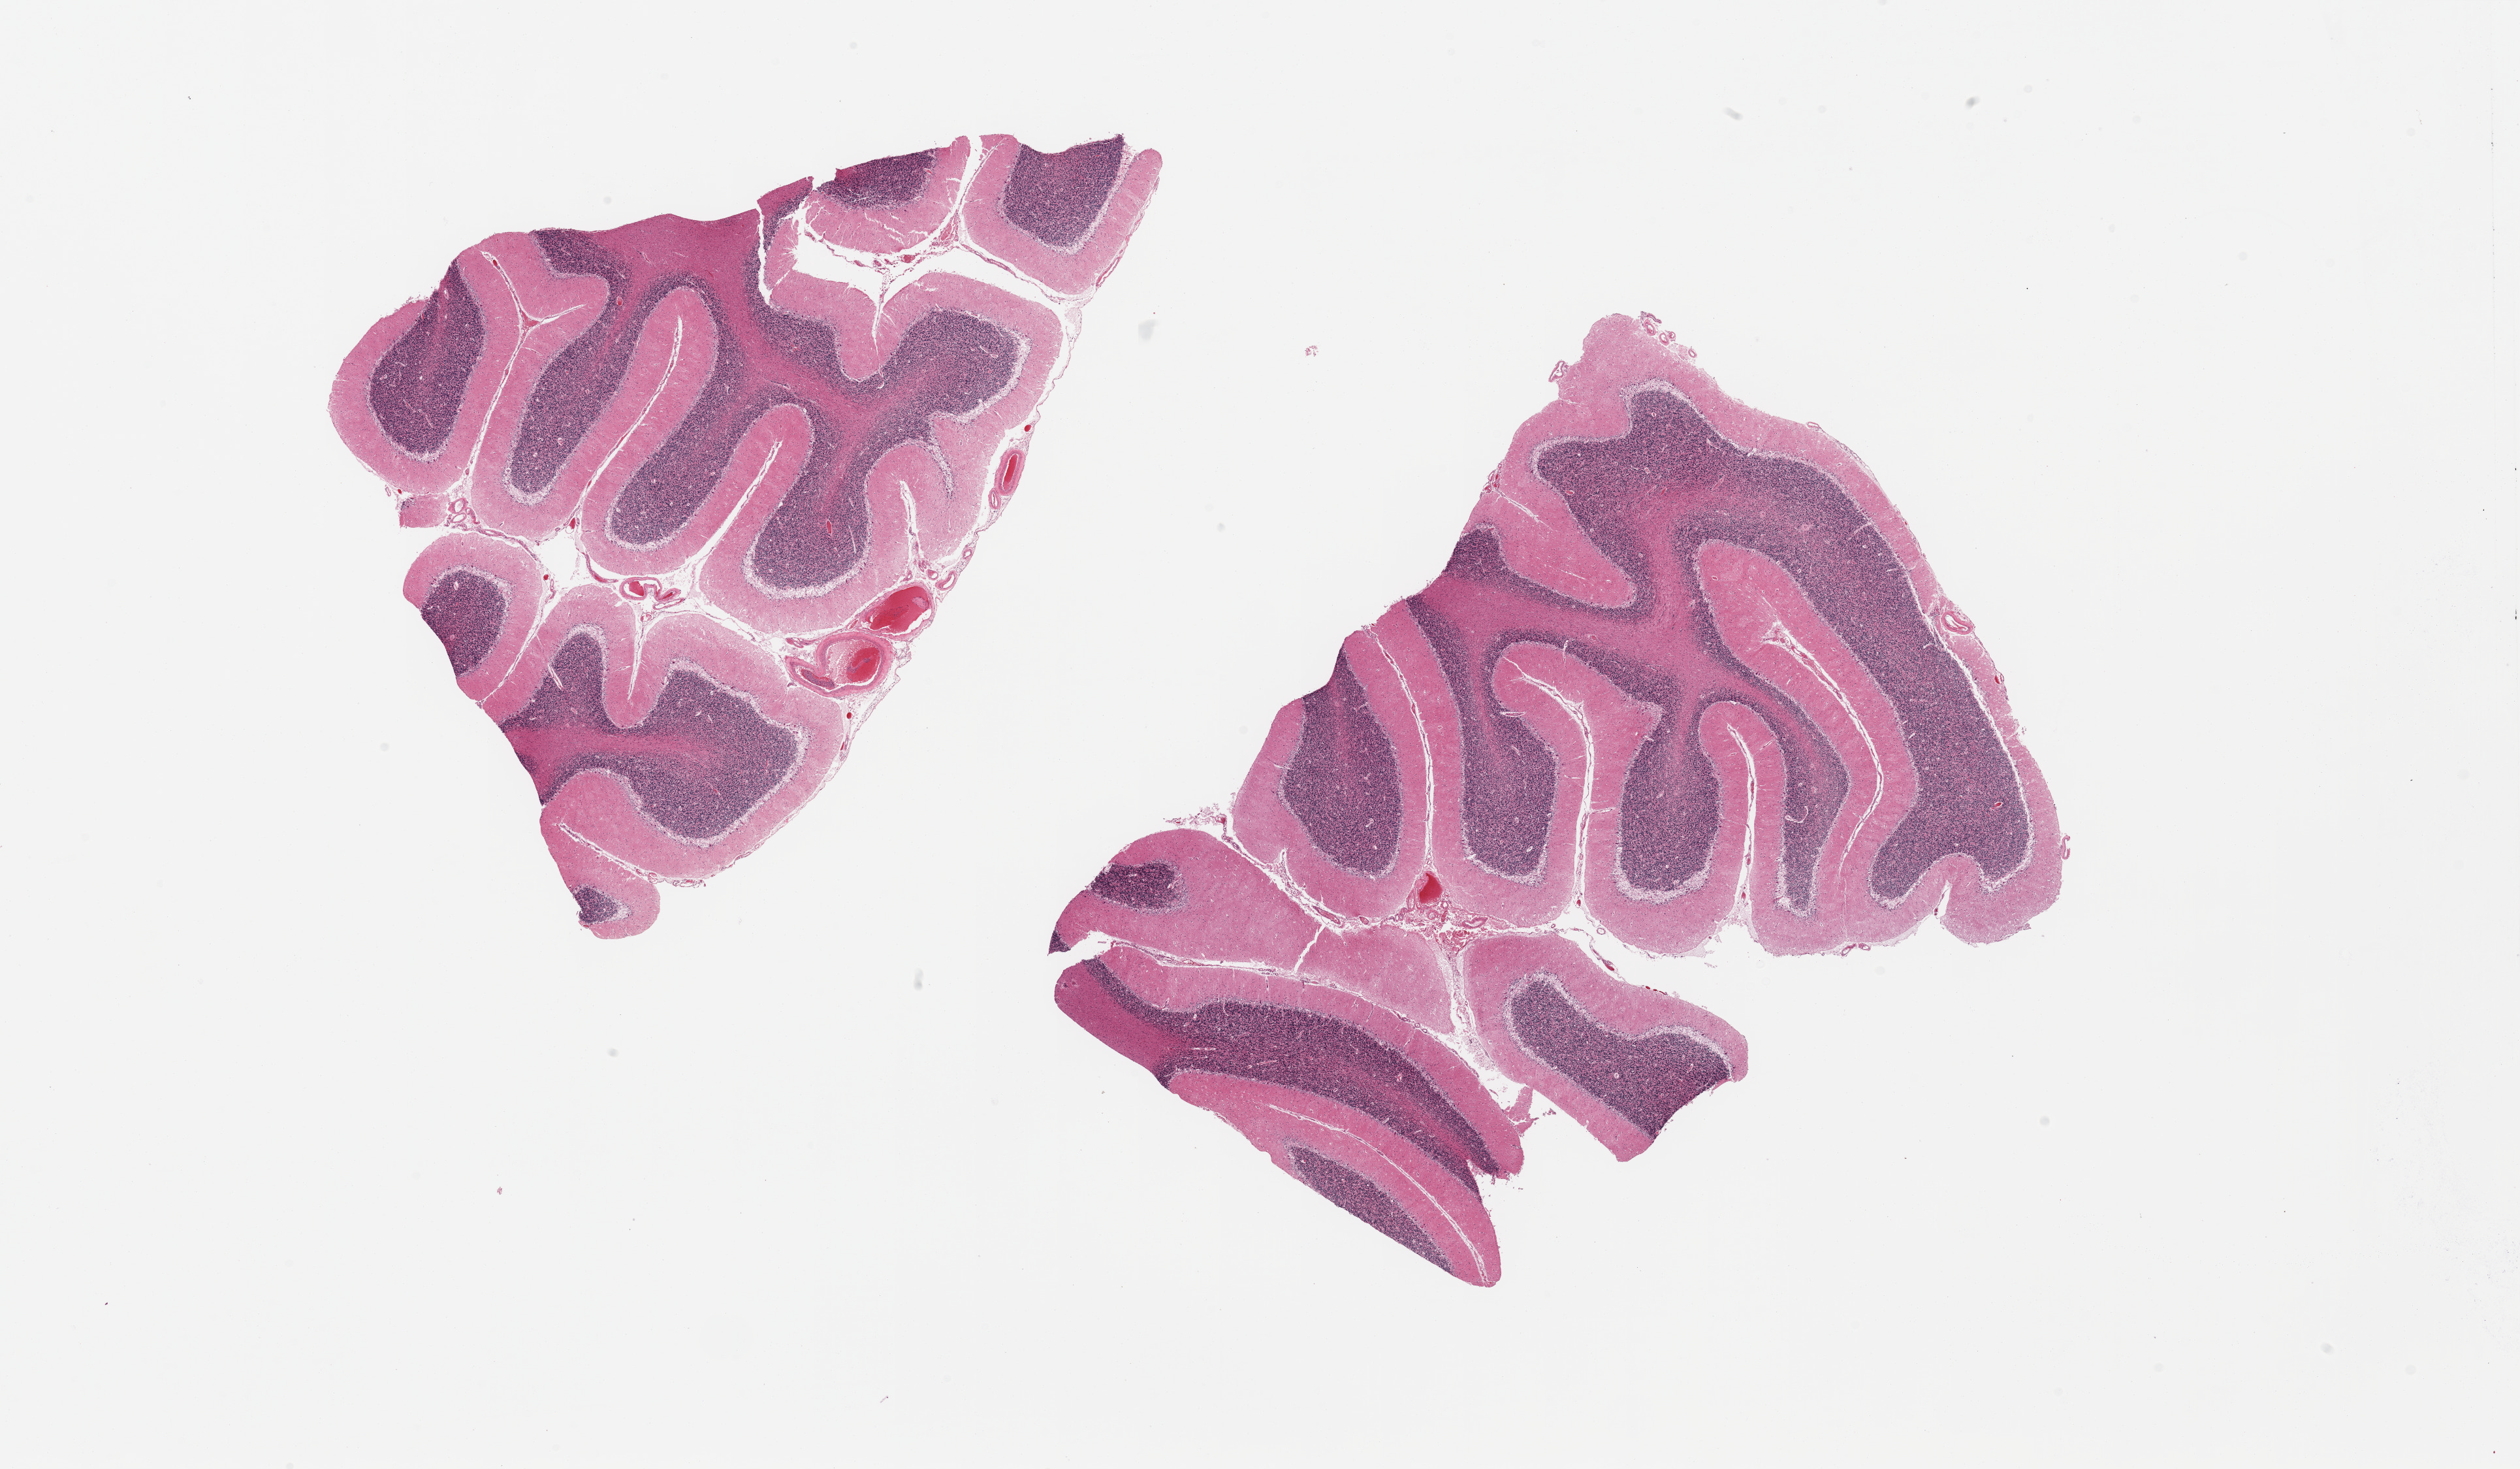
Whole-slide image, H&E stain, whole scanned area (about 30.5 x 17.8 mm, from a 20x scan) shown as a low-resolution overview; PAXgene-fixed paraffin-embedded (PFPE) section; target tissue: cerebellum; donor tissue sample. Donor sex: male.
Pathologist's review note for this sample: 2 pieces.